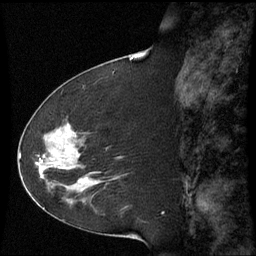
Breast MRI (dynamic contrast-enhanced), one sagittal slice; position 25 of 60 along the scan axis; dynamic contrast-enhanced series, image 2 of 3 at this slice position (ordered by acquisition); 1.5 T; TE 4.2 ms, TR 8.9 ms; 256 × 256 image matrix, field of view 210 × 210 mm. Patient: female, 51 years. Case-level facts recorded for this patient, not image findings: setting: breast cancer imaged before/during neoadjuvant chemotherapy; receptor status: HR-positive, HER2-negative.
Annotated regions visible in this slice (semi-automatically segmented with operator editing):
- analysis volume of interest (the breast-tissue region the enhancement analysis was run in; not a lesion): bounding box <50,126,102,187> (left, top, right, bottom; pixels)
- tumour enhancement mask (voxels above the 70 % enhancement threshold inside the analysis volume of interest): <52,126,98,184>